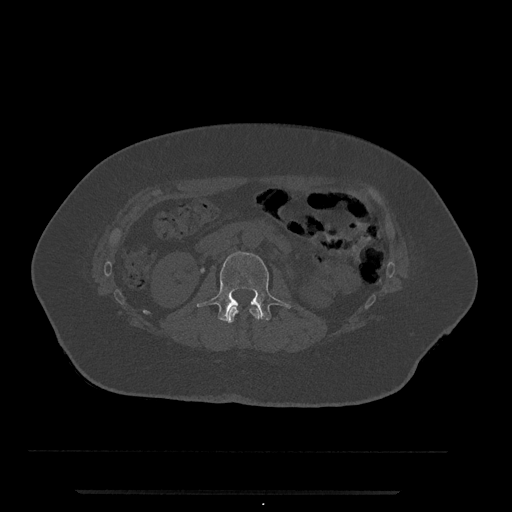
CT including the spine, one axial slice; slice 49 of 797 in the series (ordered by position); 120 kVp; bone window (W 1800 / L 400 HU); 512 × 512 image matrix. Female patient, age 51 years. From the clinical record (not read from this slice): primary cancer: neuro.
Structures marked on this image (semi-automatically segmented with operator editing):
- L1 vertebra: box from (x=226, y=306) to (x=261, y=324) px
- L2 vertebra: (x=197, y=251)–(x=291, y=322)